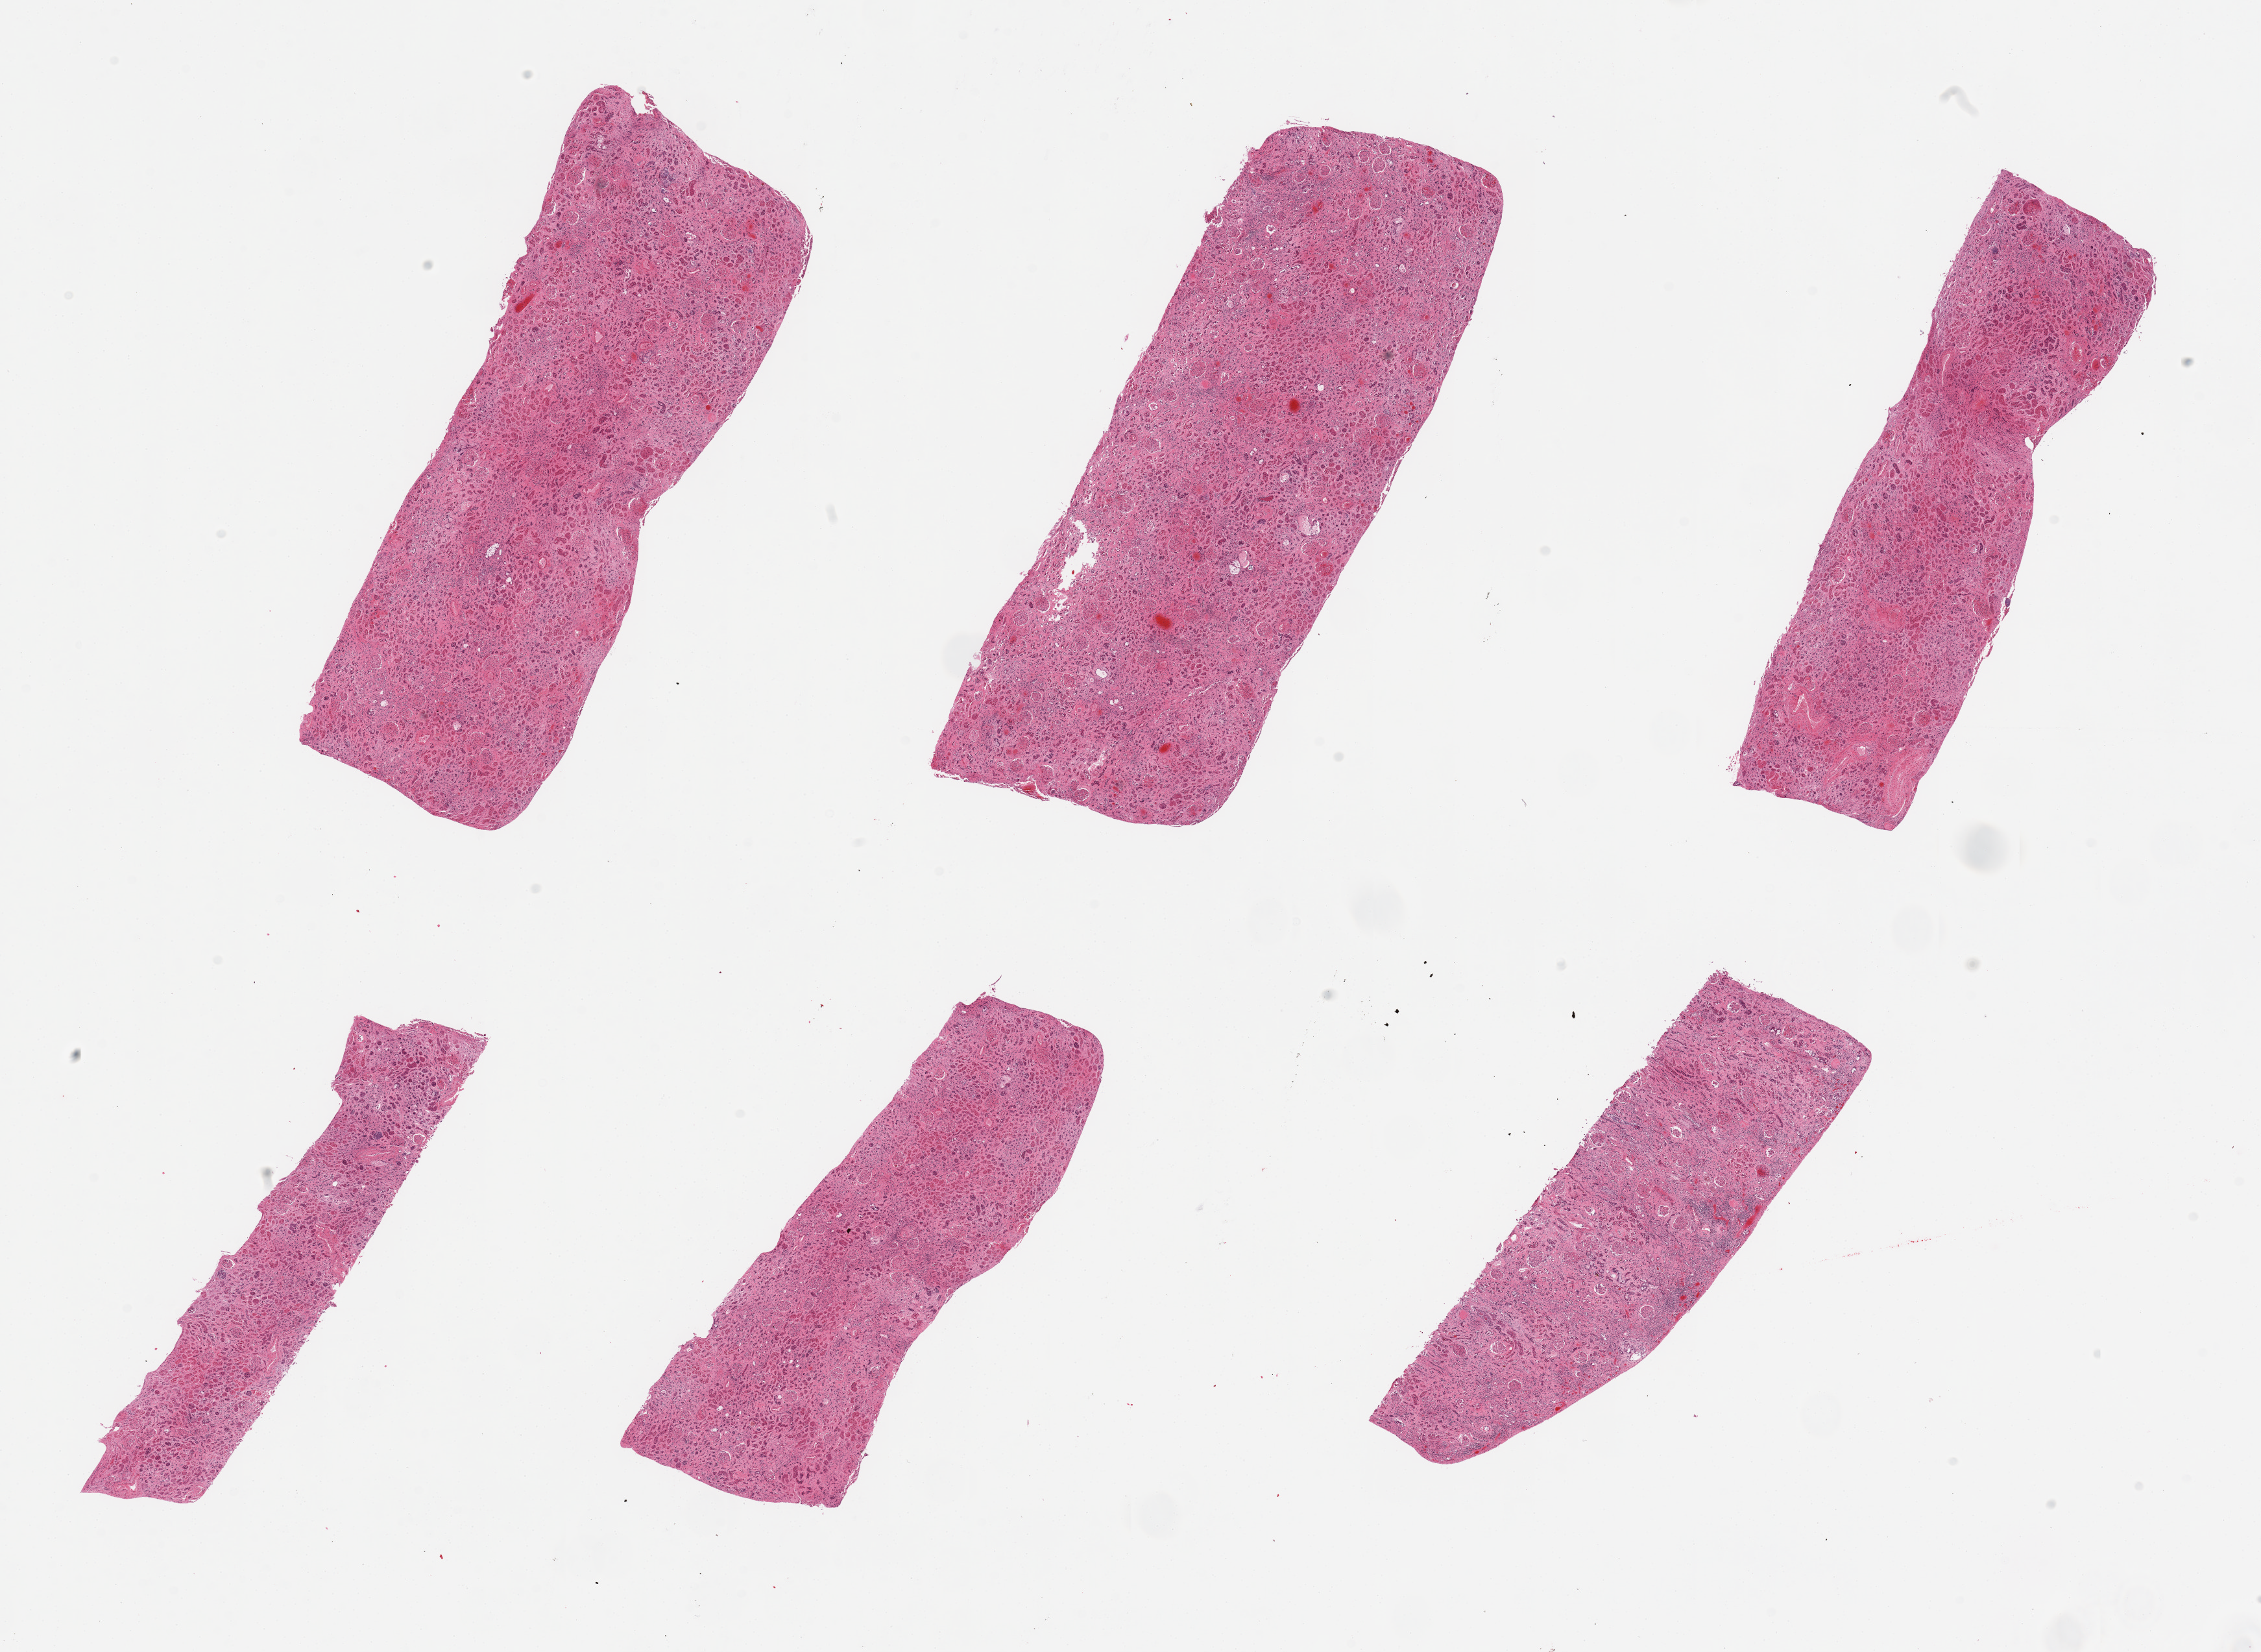
Digitized H&E-stained section — a low-resolution overview of the entire scanned area, about 27.6 x 20.1 mm (slide scanned at 20x), PAXgene-fixed, paraffin-embedded tissue, target tissue: renal cortex, donor tissue sample. Donor sex: male.
* reviewer comment on this tissue sample: 6 pieces